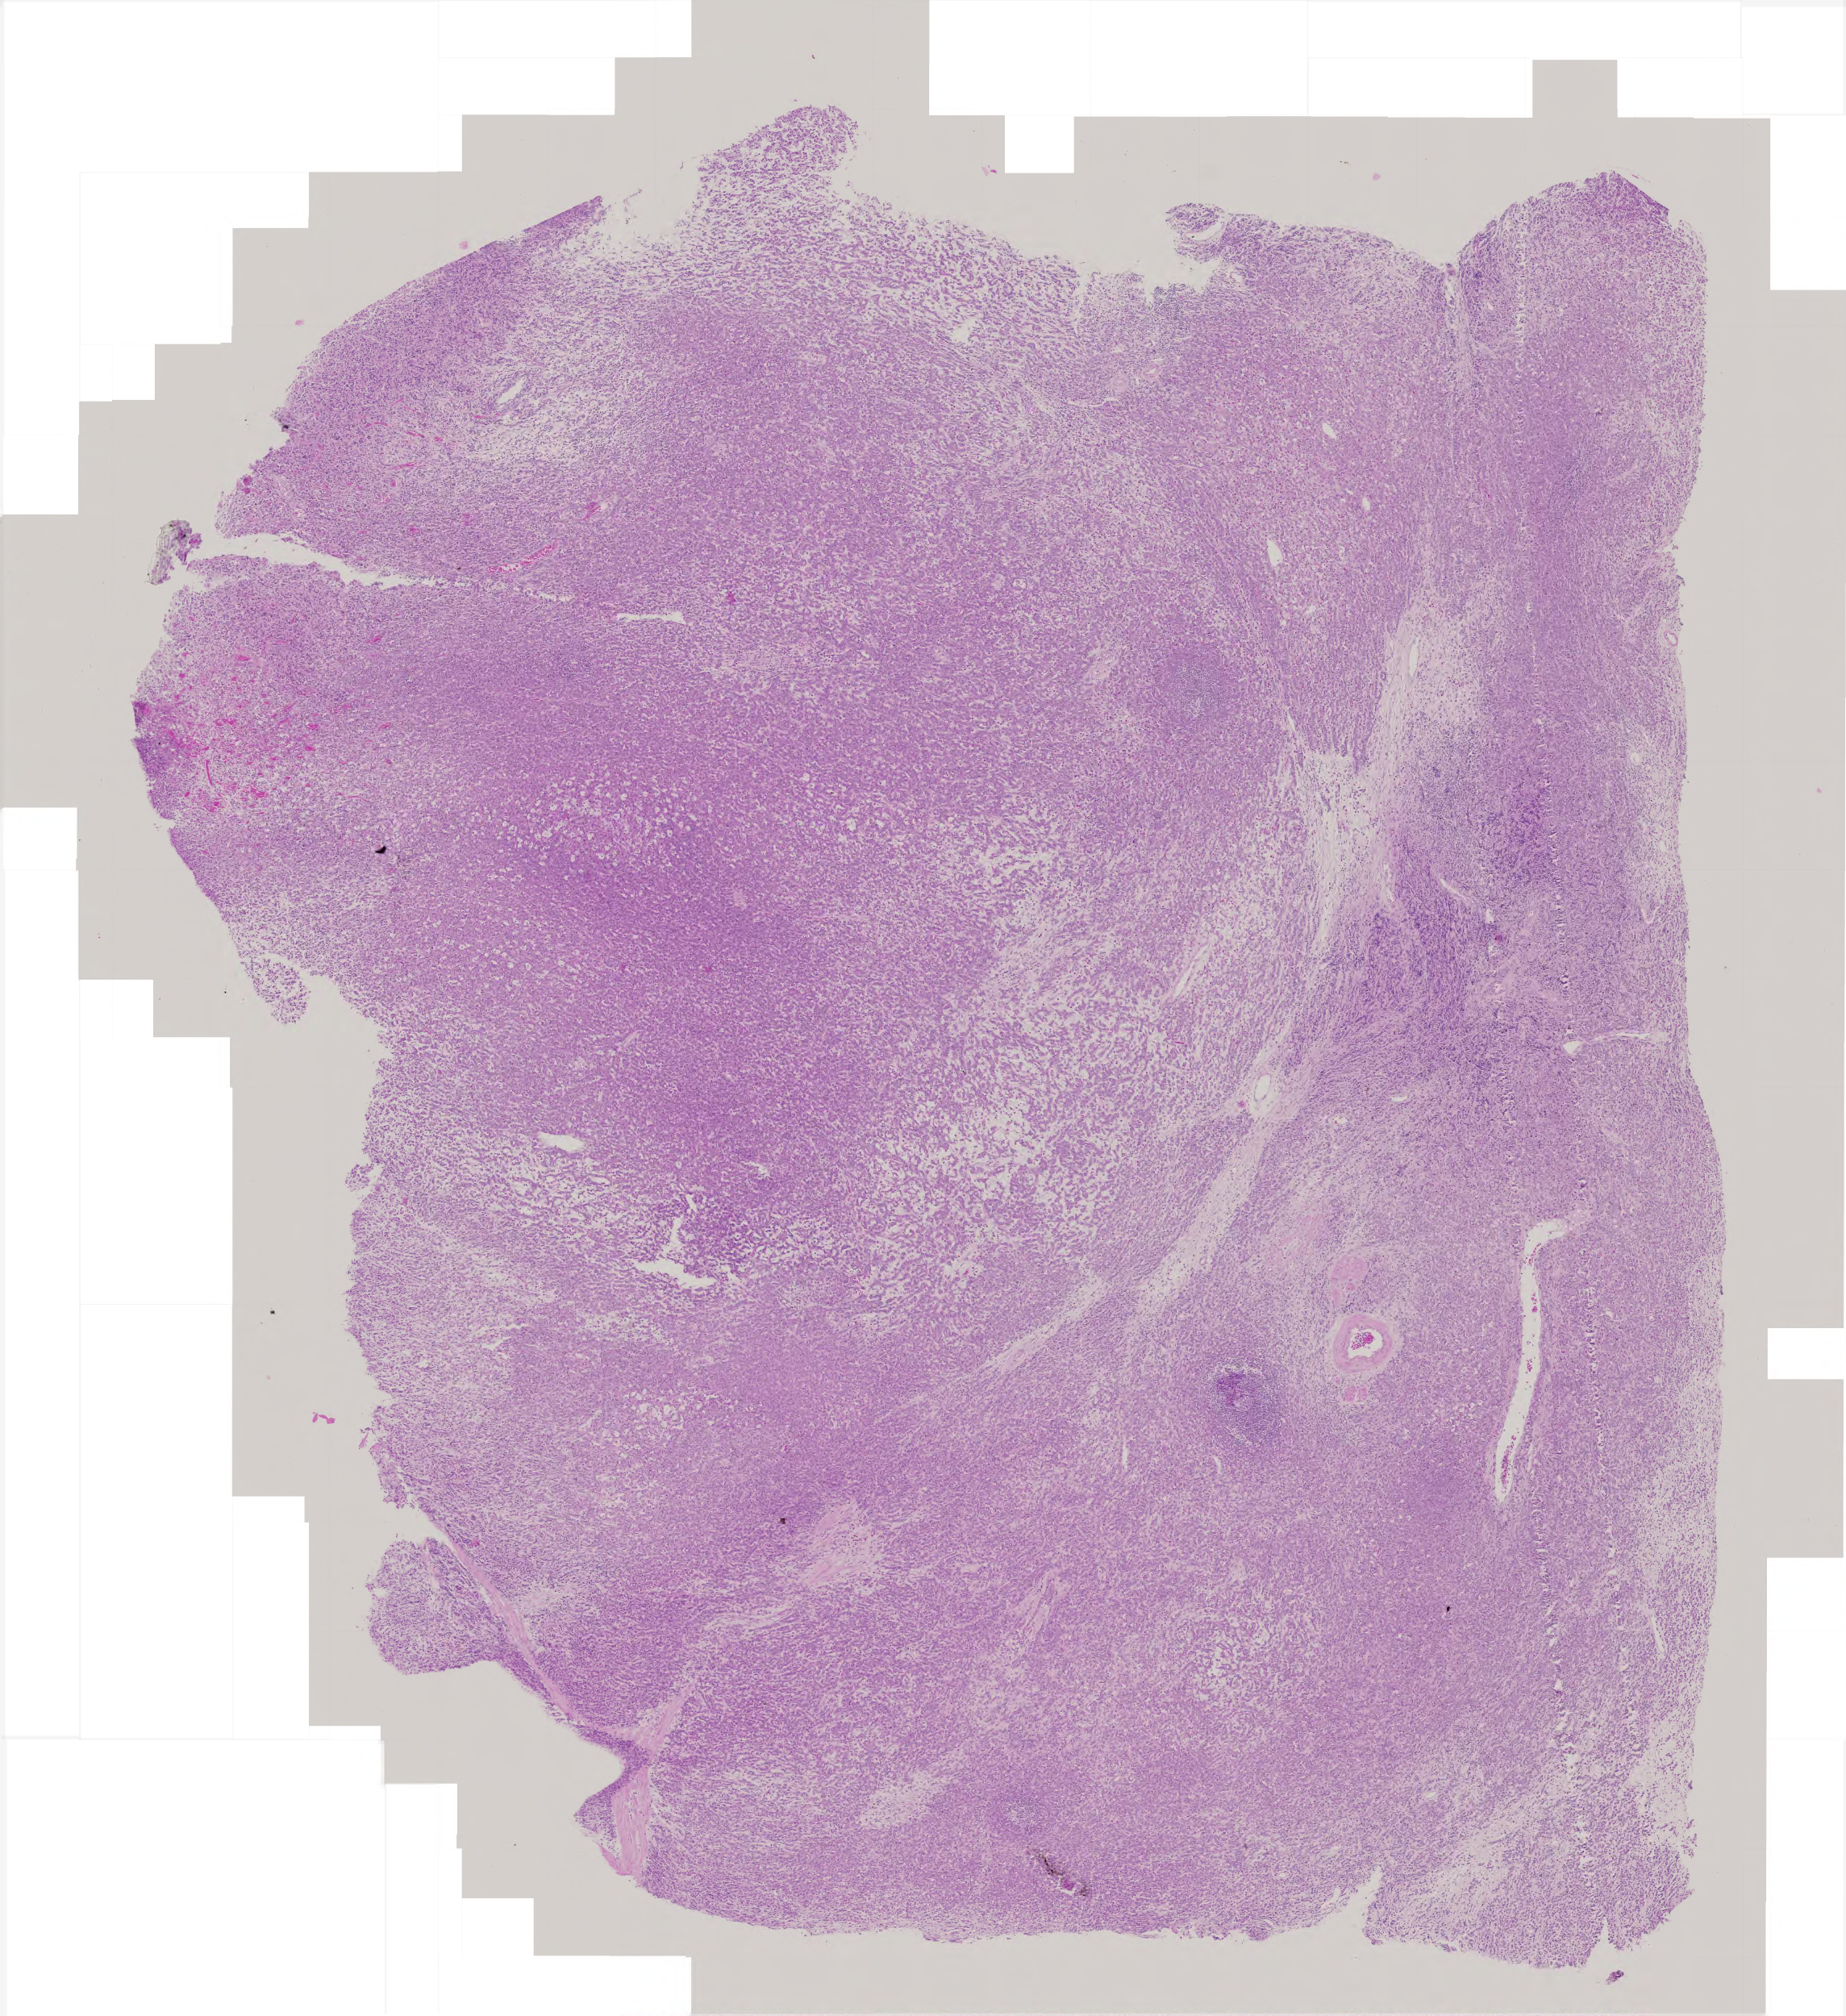
Digitized H&E-stained tissue section (whole slide) — a low-resolution overview of the entire scanned area, about 4.6 x 5.0 mm, FFPE section, sample: primary tumour, stomach. Male, age 71 years at initial diagnosis. Histologic grade: G3 (poorly differentiated).
Lymph nodes positive (case pathology): 0 of 60 examined. Diagnosis: Adenocarcinoma, NOS (cardia, NOS). TNM: T2 N0 M0. AJCC pathologic stage: IB (5th edition).